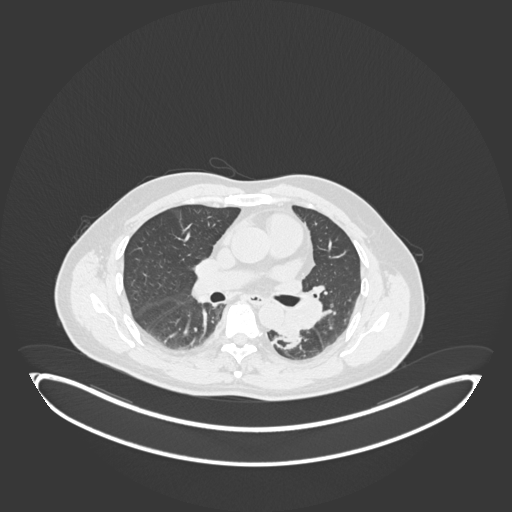
Chest CT, one axial slice. Position 112 of 258 along the scan axis. Reconstruction kernel B30f. 120 kVp. Lung window (W 1500 / L -600 HU). 512 × 512 image matrix, field of view 500 × 500 mm. Male patient, age 54 years. Case-level facts recorded for this patient, not image findings: clinical TNM (as recorded): T3 N0 M0.
Structures marked on this image (rectangle marked by the reading radiologist):
- lung tumour (recorded histology: squamous cell carcinoma): bounding box (x1, y1, x2, y2) in pixels: (277, 305, 302, 348)